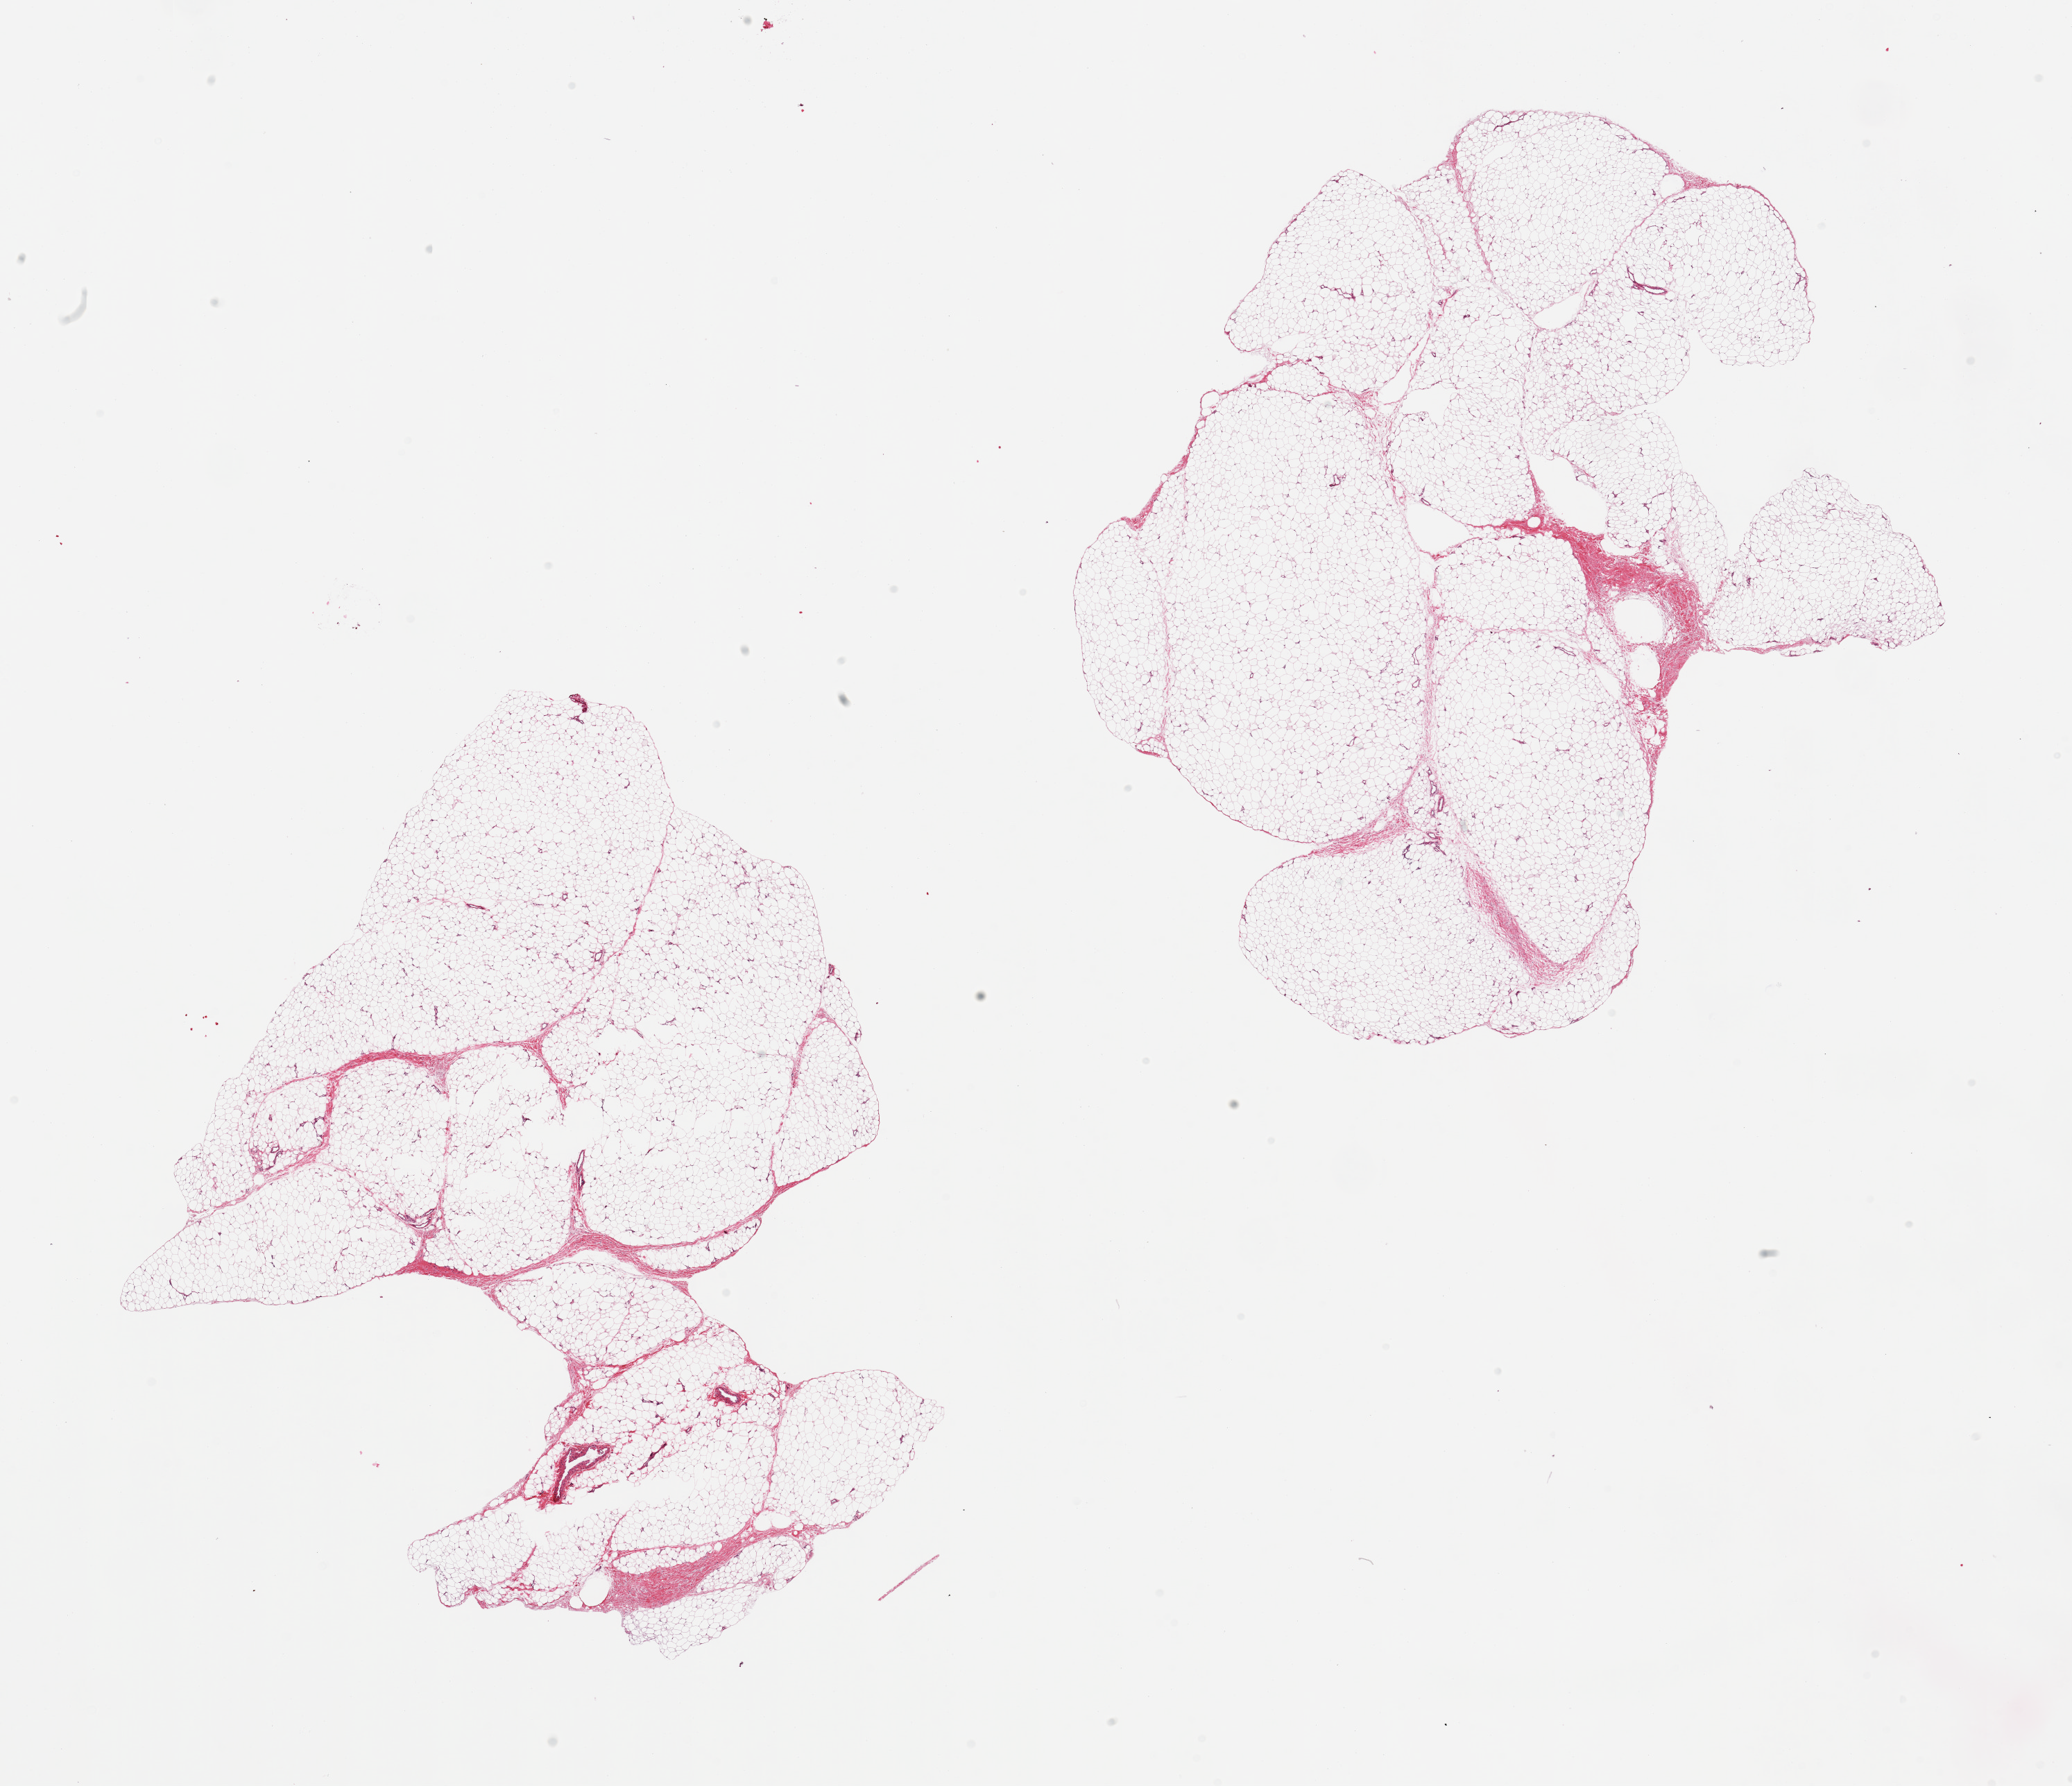
Whole-slide image, H&E stain, brightfield — low-resolution overview of the scanned area, about 23.6 x 20.4 mm (acquisition: 20x scan). PAXgene-fixed, paraffin-embedded tissue. Sampled site (target tissue): adipose tissue. Donor tissue sample. Donor: male.
* review note (as recorded): 2 pieces